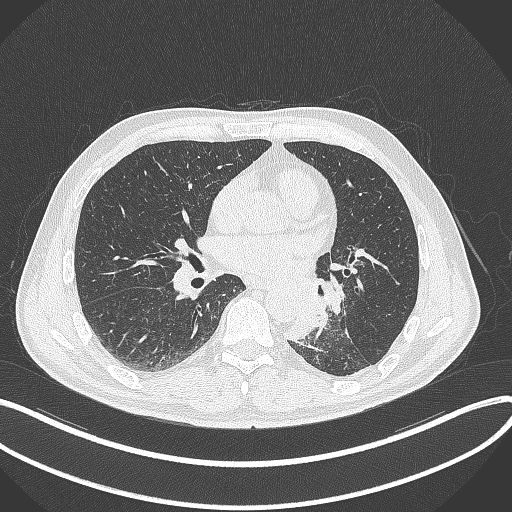
Chest CT, one axial slice. Reconstruction kernel B70f. 120 kVp. Lung window (W 1500 / L -600 HU). 1 mm slice thickness. 512 × 512 image matrix, field of view 400 × 400 mm. Patient: male, 59 years. From the clinical record (not read from this slice): clinical TNM (as recorded): T2a N2 M0.
Annotated regions visible in this slice (rectangle marked by the reading radiologist):
- lung tumour (recorded histology: squamous cell carcinoma): box from (x=282, y=289) to (x=330, y=342) px